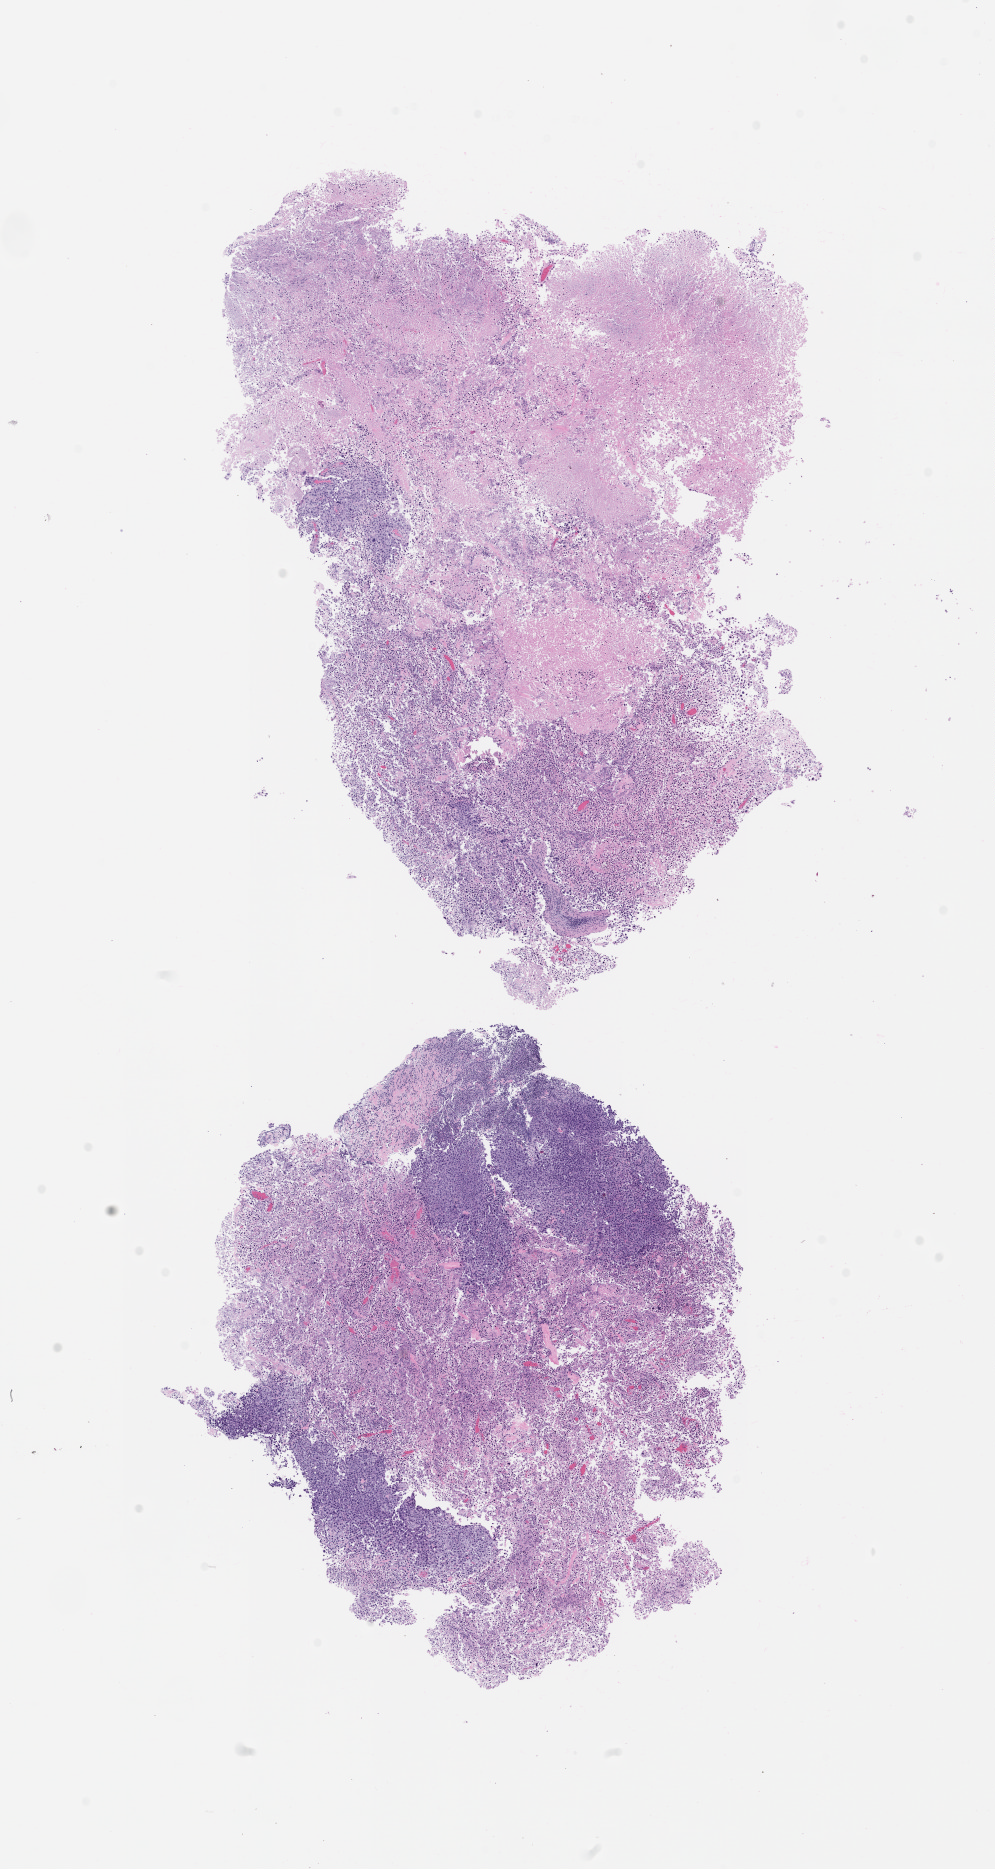
Whole-slide image, hematoxylin and eosin (H&E) stain of the patient's (originator) tumor tissue — whole scanned area (about 8.0 x 15.0 mm) shown as a low-resolution overview; FFPE section; originating tumor site category: head and neck. Patient: male, 88 years old.
Diagnosis: Head and Neck Squamous Cell Carcinoma.